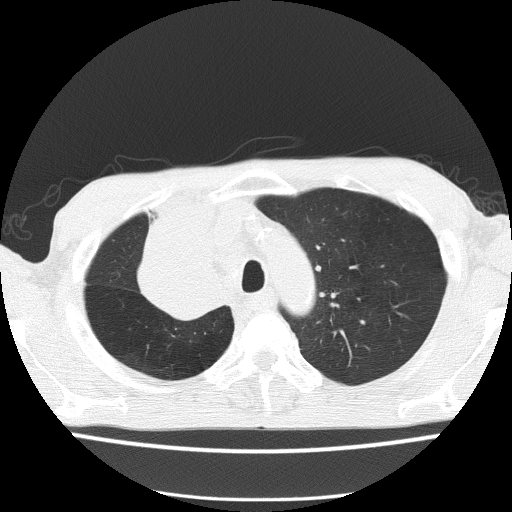
Low-dose screening chest CT, axial slice, first (baseline) screen, lung window (W 1500 / L -600 HU), 2 mm slice thickness. Male participant, aged 59 years at enrolment. Former smoker at enrolment.
Lesion marked by an expert reader, bounding box [x1, y1, x2, y2] px = [130, 235, 239, 327]. The screening reader recorded 5 non-calcified nodules or masses ≥4 mm on this exam (left upper lobe, left upper lobe, left upper lobe, right middle lobe, right lower lobe); which of them this box marks is not recorded.